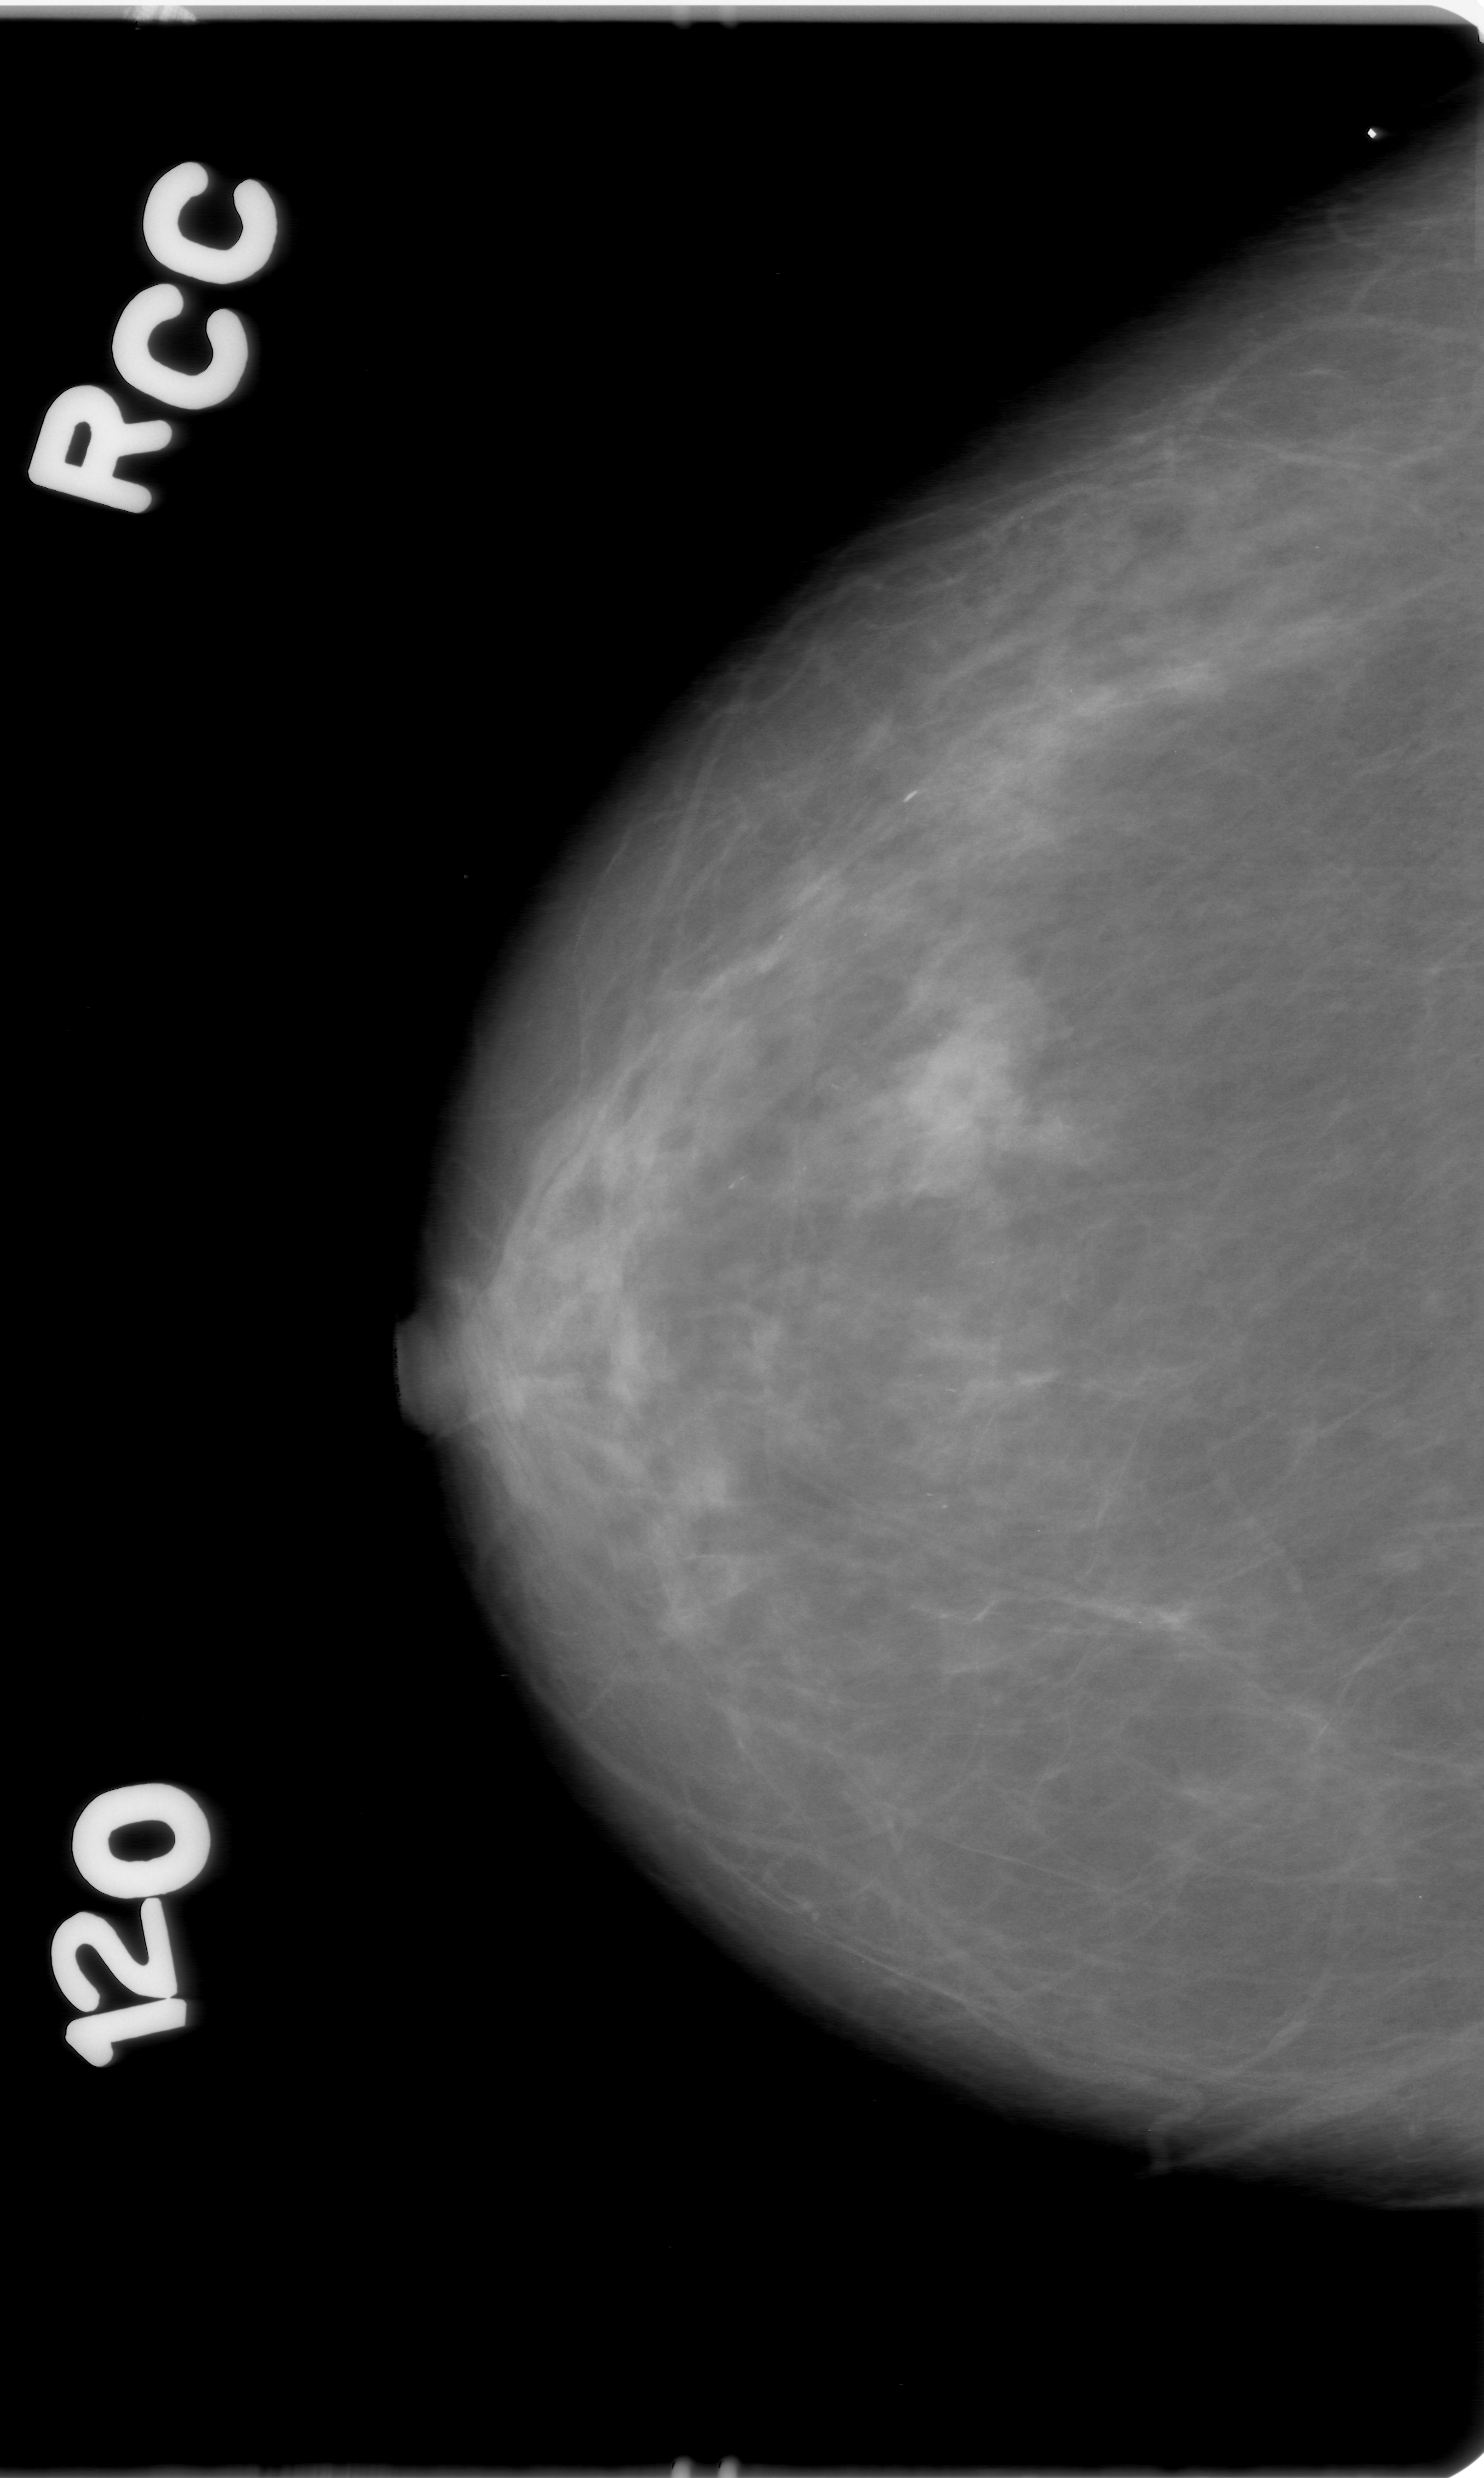
Mammogram (digitized film), right breast, craniocaudal (CC) view.
Finding: mass, shape lobulated, margins obscured; BI-RADS assessment category 0; subtlety rating 3 on a 1 (subtle) to 5 (obvious) scale; pathology result (as recorded, not read from the image): benign.